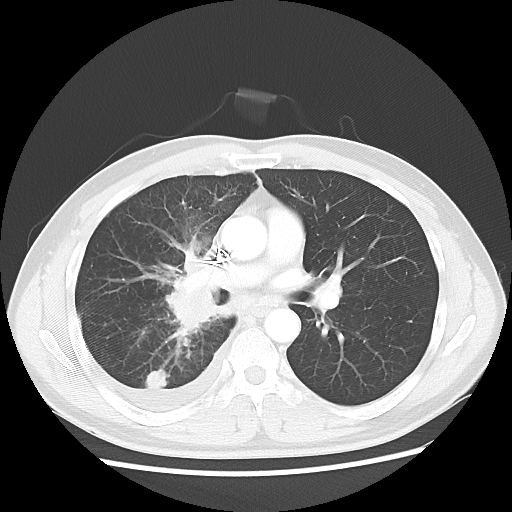
Chest CT, one axial slice; position 30 of 56 along the scan axis; lung window (W 1500 / L -600 HU); 5 mm slice thickness; 512 × 512 image matrix, field of view 360 × 360 mm. Patient: male, 46 years. Case-level facts recorded for this patient, not image findings: clinical TNM (as recorded): T2 N3 M1.
Annotated regions visible in this slice (rectangle marked by the reading radiologist):
- lung tumour (recorded histology: adenocarcinoma): bounding box <154,237,226,332> (left, top, right, bottom; pixels)